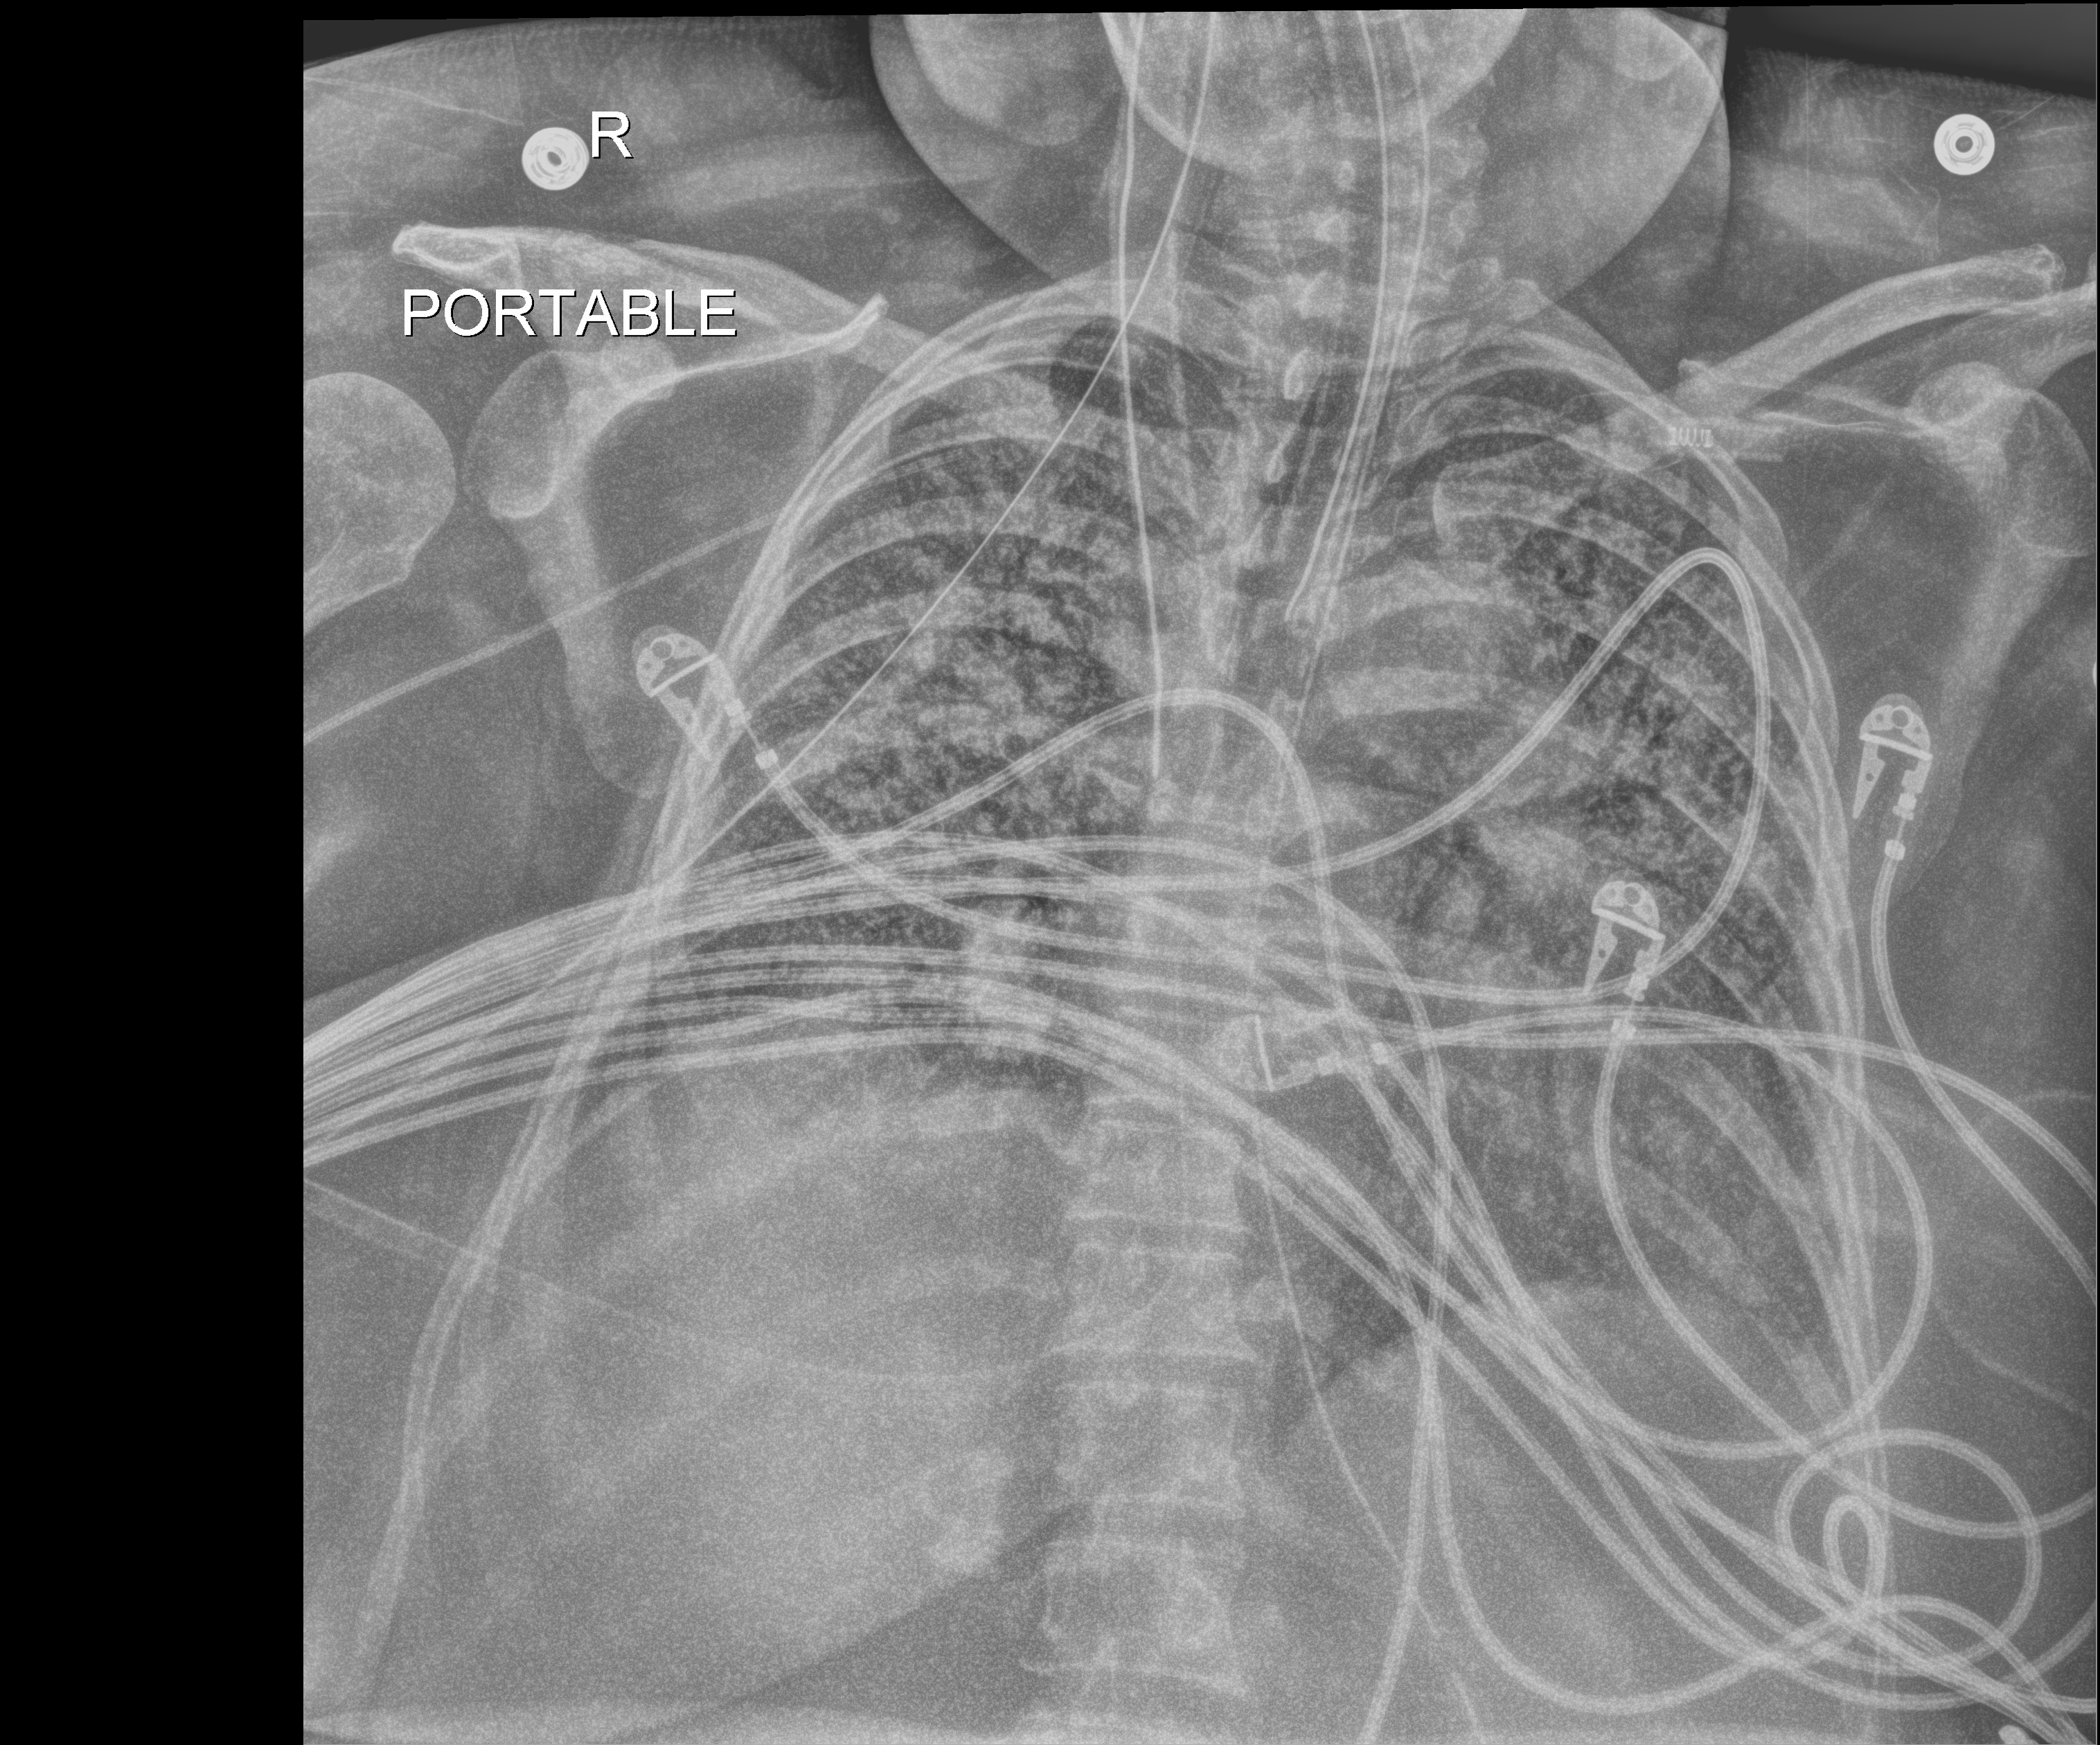
Chest X-ray (portable). Female patient hospitalised with COVID-19, age 18–59 years.
From the hospital-stay record, not from the radiograph (when in the stay this image was taken is not recorded): mechanically ventilated during this hospital stay: yes.